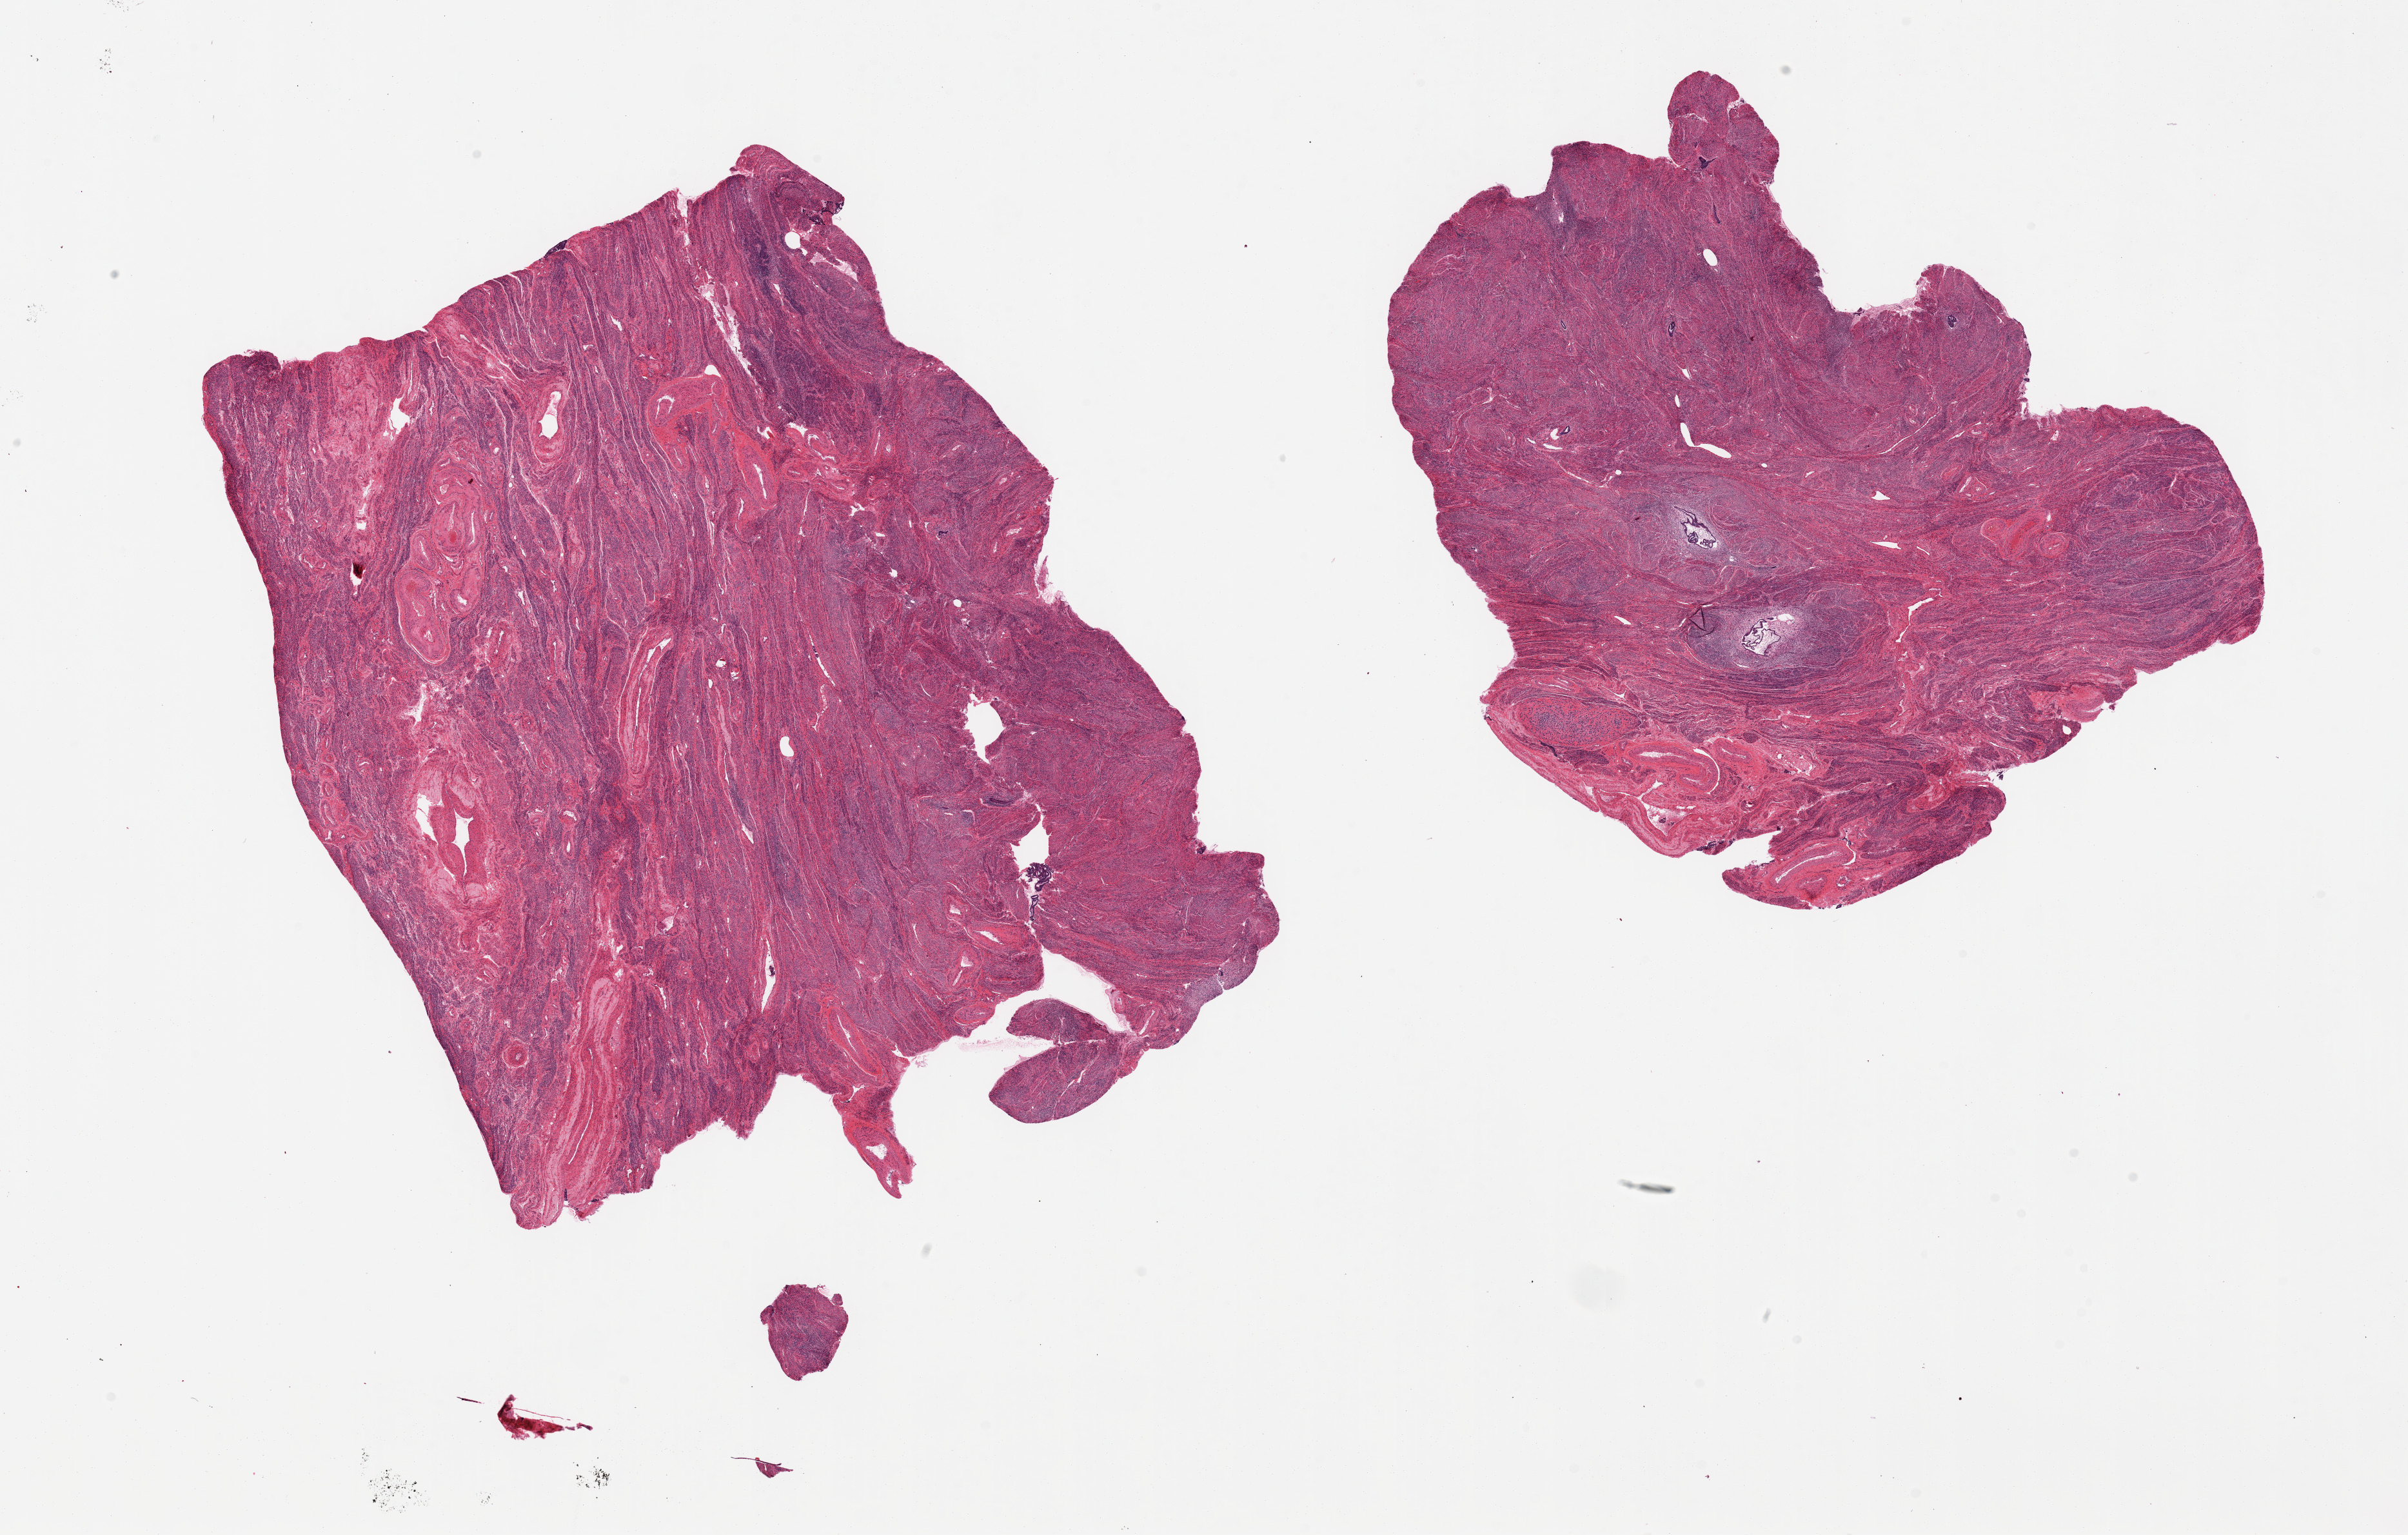
Whole-slide image, haematoxylin and eosin stain, brightfield — shown as a low-resolution overview of the whole scanned area (about 29.5 x 18.8 mm); PAXgene-fixed, paraffin-embedded tissue; sampled site (target tissue): uterus; tissue donor sample. Donor: female.
* review note (as recorded): 2 pieces, predominantly myometrium with strips of endometrial glands, focal adenomyosis, microscopic leiomyoma